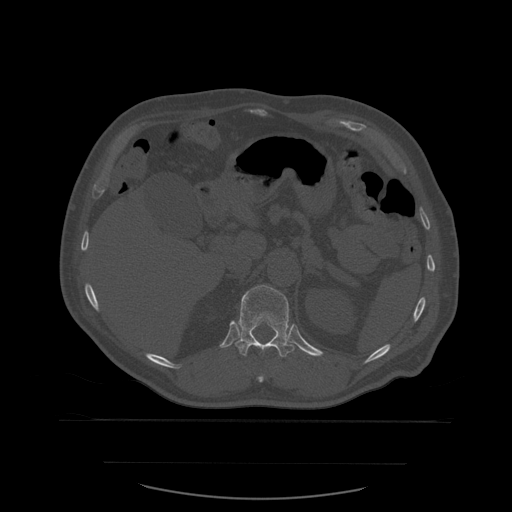
CT including the spine, one axial slice; position 275 of 590 along the scan axis; bone window (W 1800 / L 400 HU); 1.25 mm slice thickness; 512 × 512 image matrix, field of view 479 × 479 mm. Patient age 71 years. From the clinical record (not read from this slice): primary cancer: lung; vertebrae with lytic lesions (as recorded): T1, T2, L5, S1.
Annotated regions visible in this slice (semi-automatic segmentation, software-assisted and operator-edited):
- T11 vertebra: bounding box (x1, y1, x2, y2) in pixels: (258, 376, 264, 383)
- T12 vertebra: (235, 285, 295, 357)